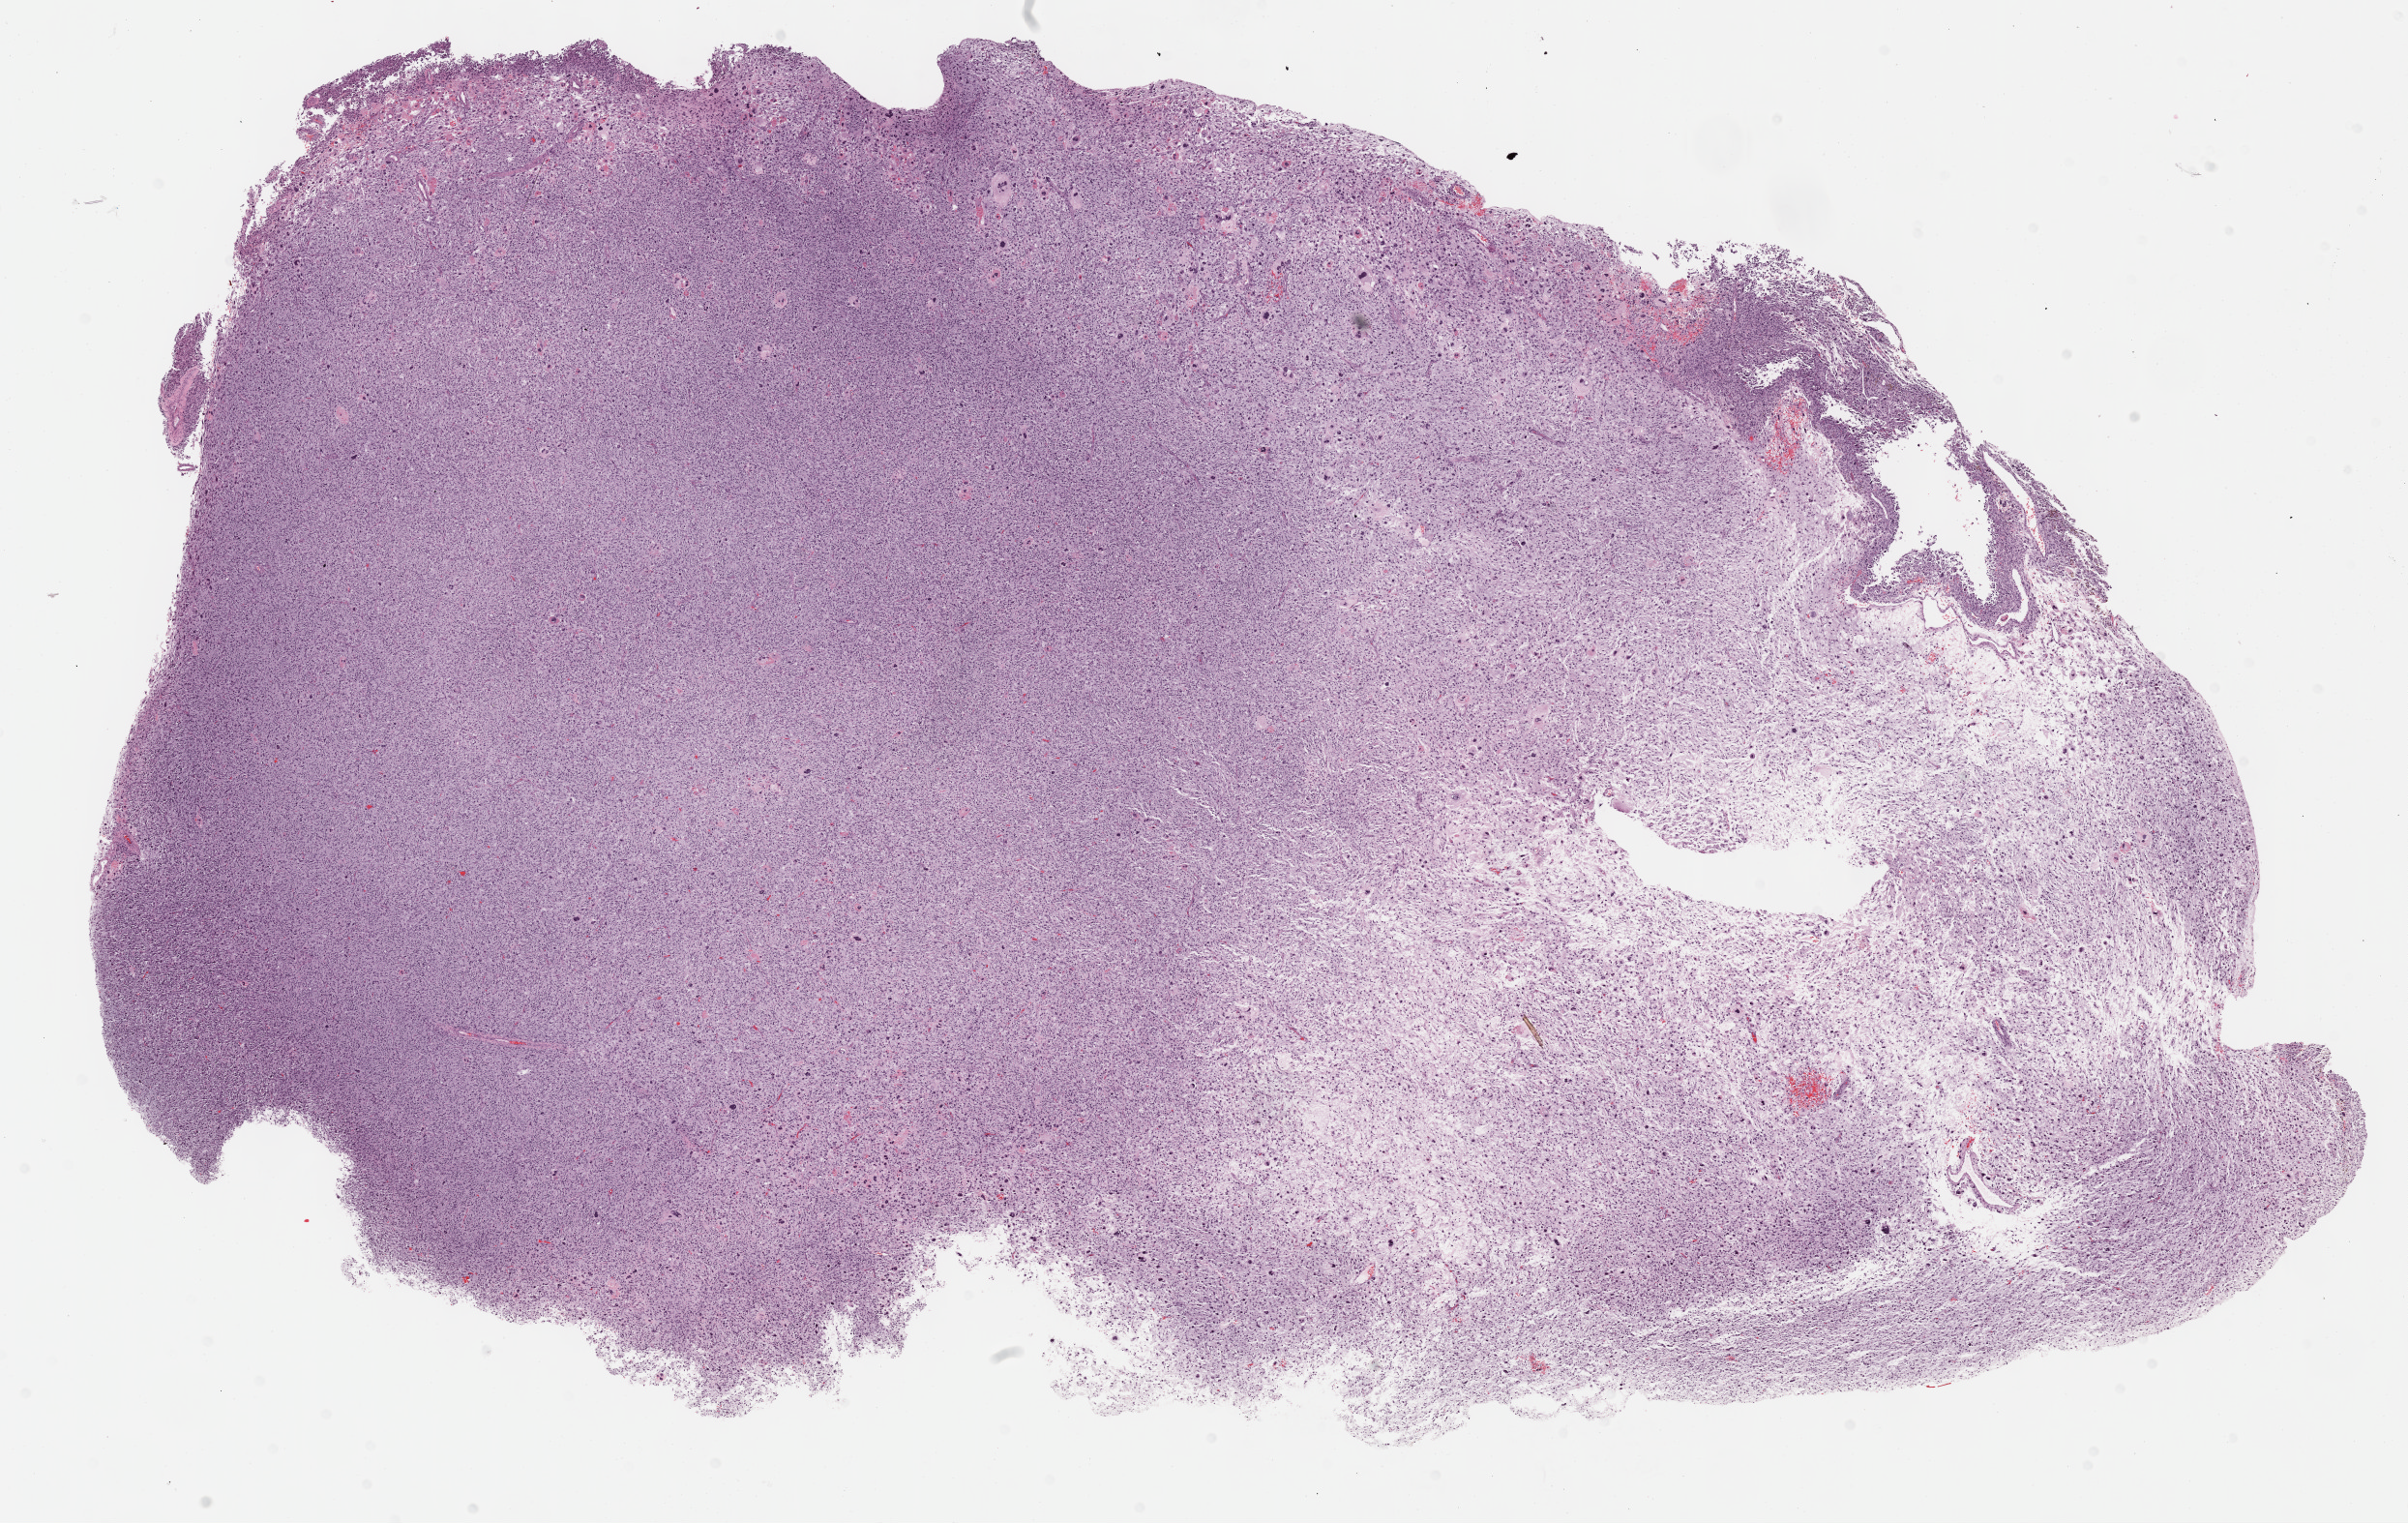
Whole-slide histology image, Hematoxylin and eosin (H&E) stained — shown as a low-resolution overview of the whole scanned area (about 20.1 x 12.7 mm, slide scanned at 40x). Formalin-fixed paraffin-embedded (FFPE) diagnostic section. Primary tumour sample from the connective, subcutaneous and other soft tissues. Patient: male, age at initial diagnosis 74 years.
Histologic diagnosis: Fibromyxosarcoma.